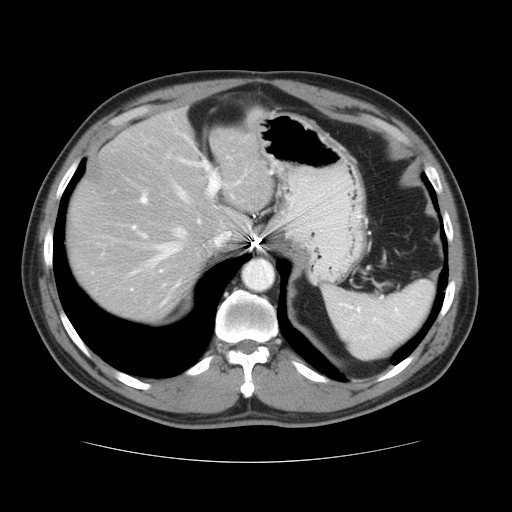
Contrast-enhanced abdominal CT, one axial slice; reconstruction kernel STANDARD; 120 kVp; intravenous contrast given; soft-tissue window (W 400 / L 40 HU); 5 mm slice thickness; 512 × 512 image matrix. Male patient, age 66 years. From the clinical record (not read from this slice): diagnosis: colorectal cancer liver metastases, imaged before liver resection; multiple liver metastases: yes; largest metastasis: 1.6 cm; disease in both lobes: yes.
Outlined on this slice (expert manual segmentation):
- hepatic veins: bounding box <134,184,232,273> (left, top, right, bottom; pixels)
- liver: <67,107,276,323>
- planned liver remnant (the part of the liver to remain after resection): <67,114,276,323>
- portal vein (with intrahepatic branches): <131,158,221,231>